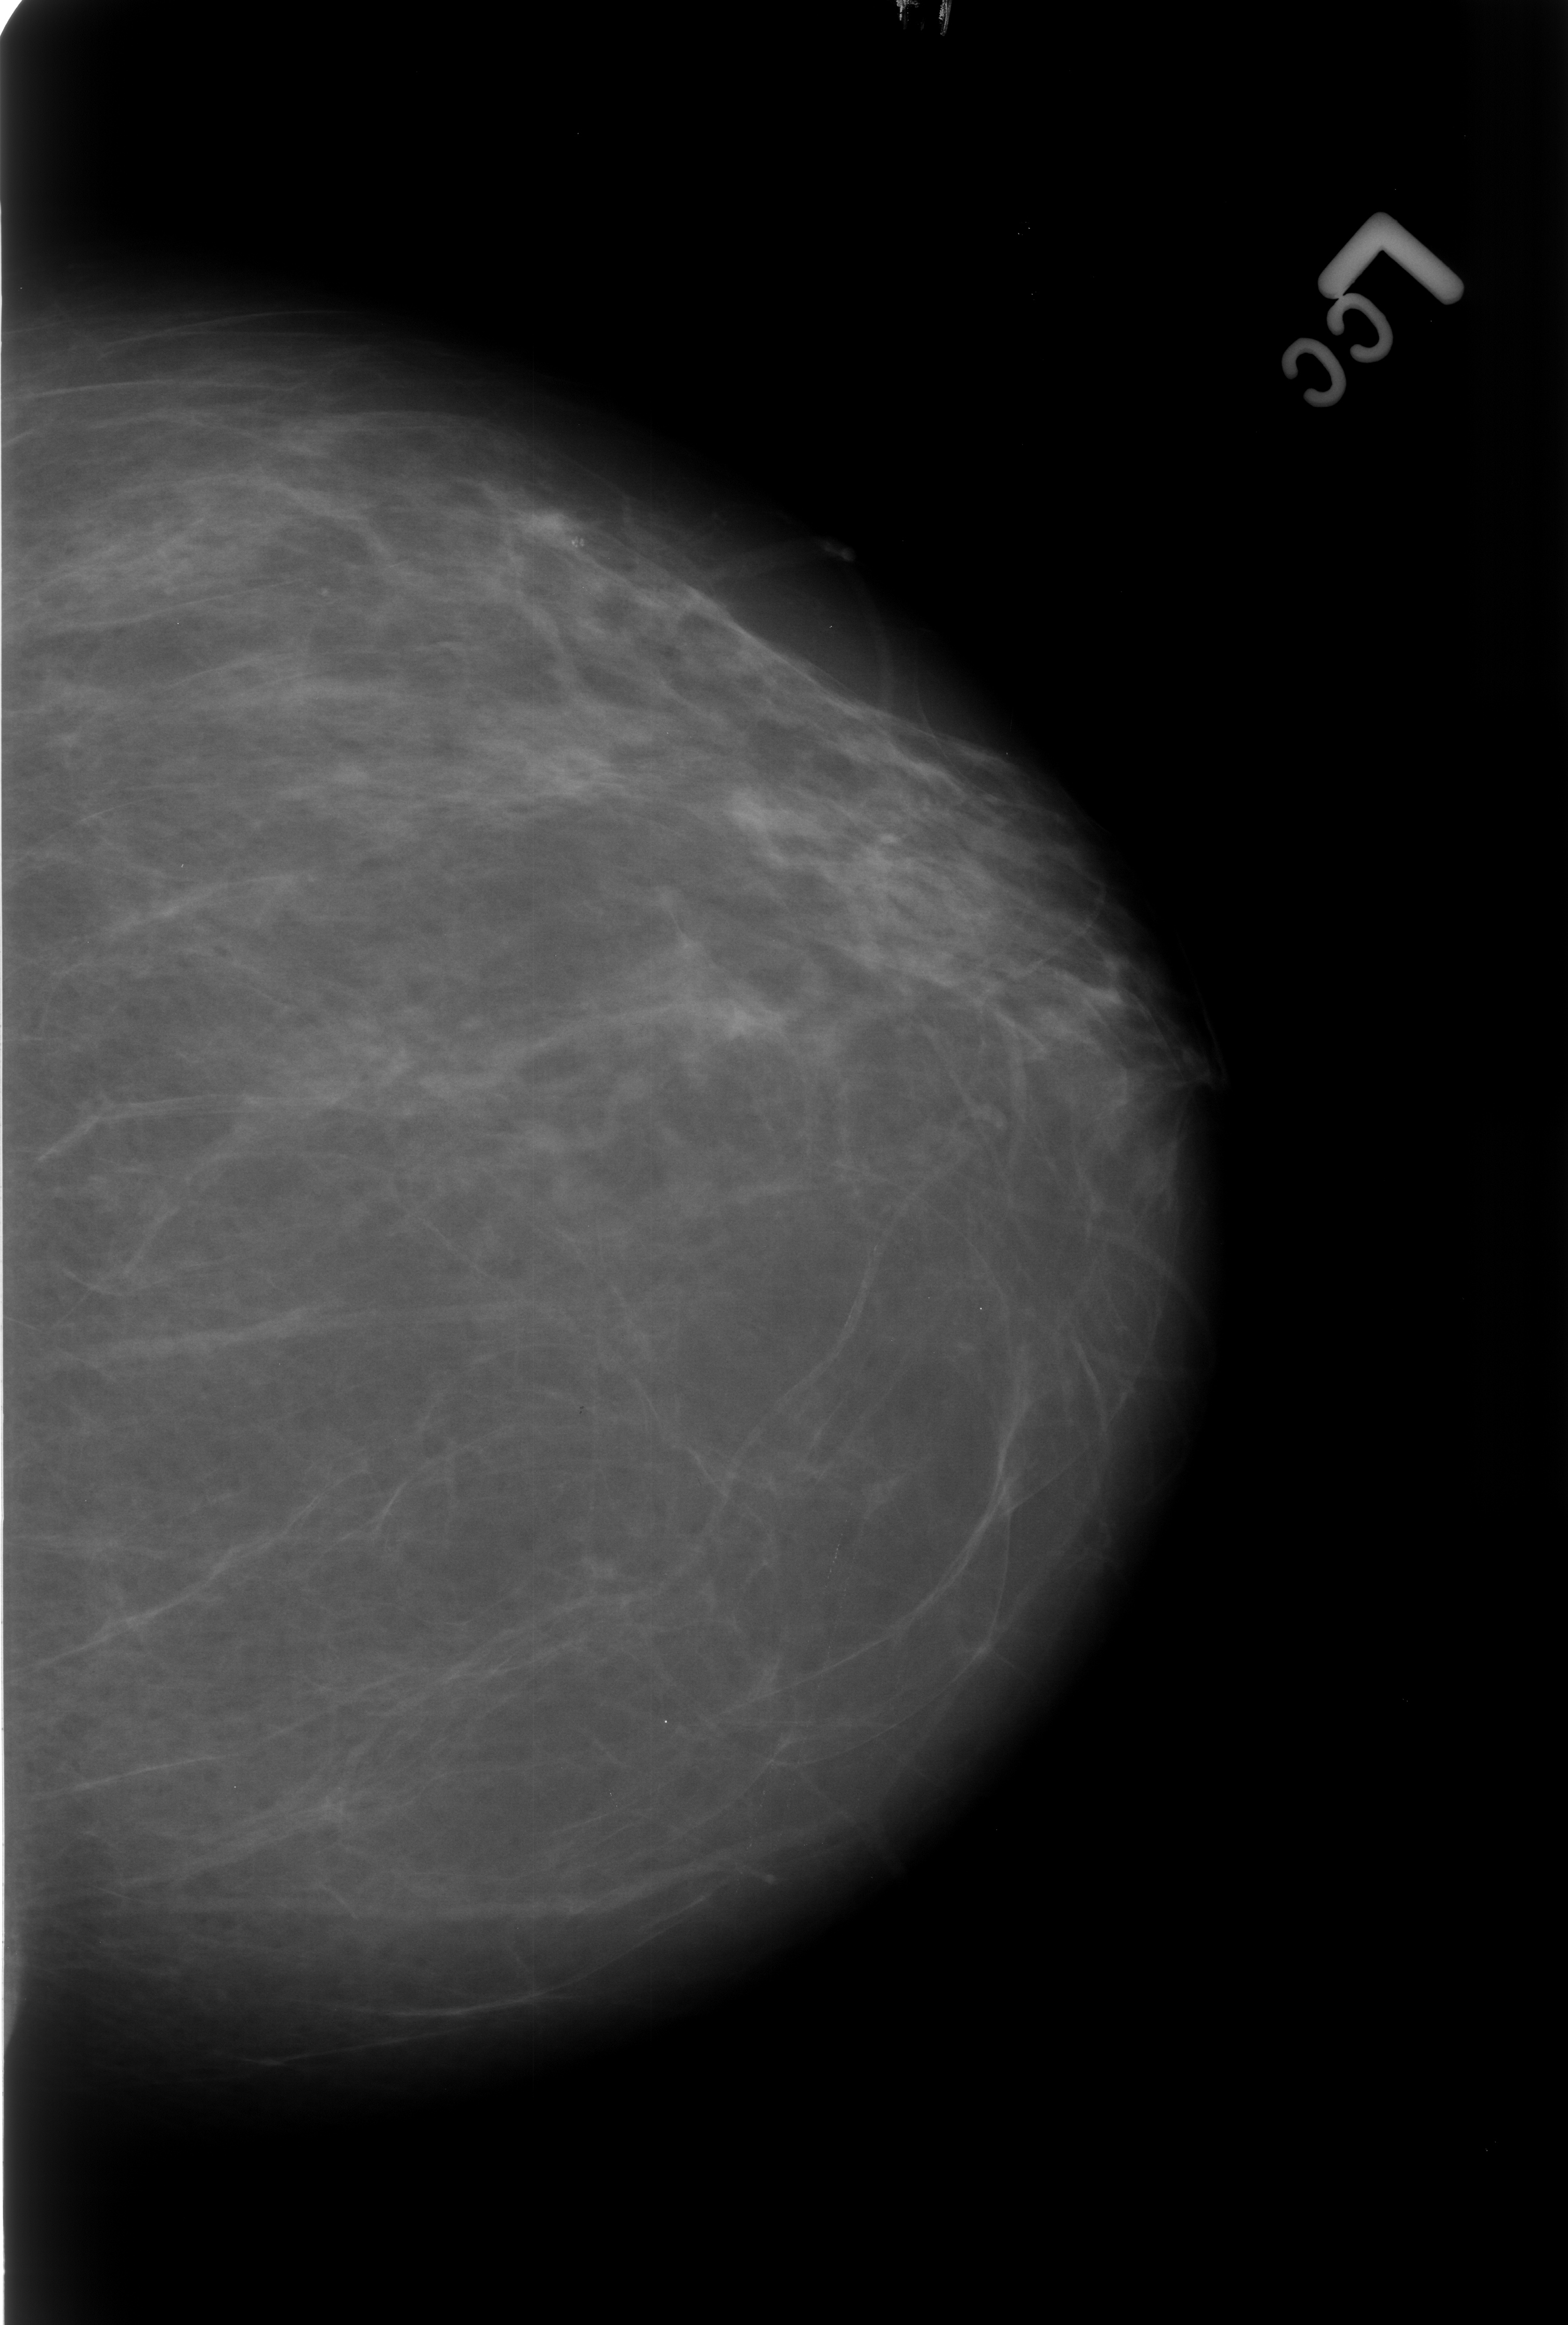
Mammogram (digitized film); left breast; craniocaudal (CC) view; breast composition: scattered fibroglandular densities (BI-RADS density category 2 of 4); 1568 × 2325 image matrix.
Expert-marked regions of interest on this image (one box per marked abnormality):
- calcifications, morphology punctate / pleomorphic, distribution clustered; BI-RADS assessment category 4; pathology (as recorded): benign: bounding box [x1, y1, x2, y2] px = [540, 511, 608, 579]